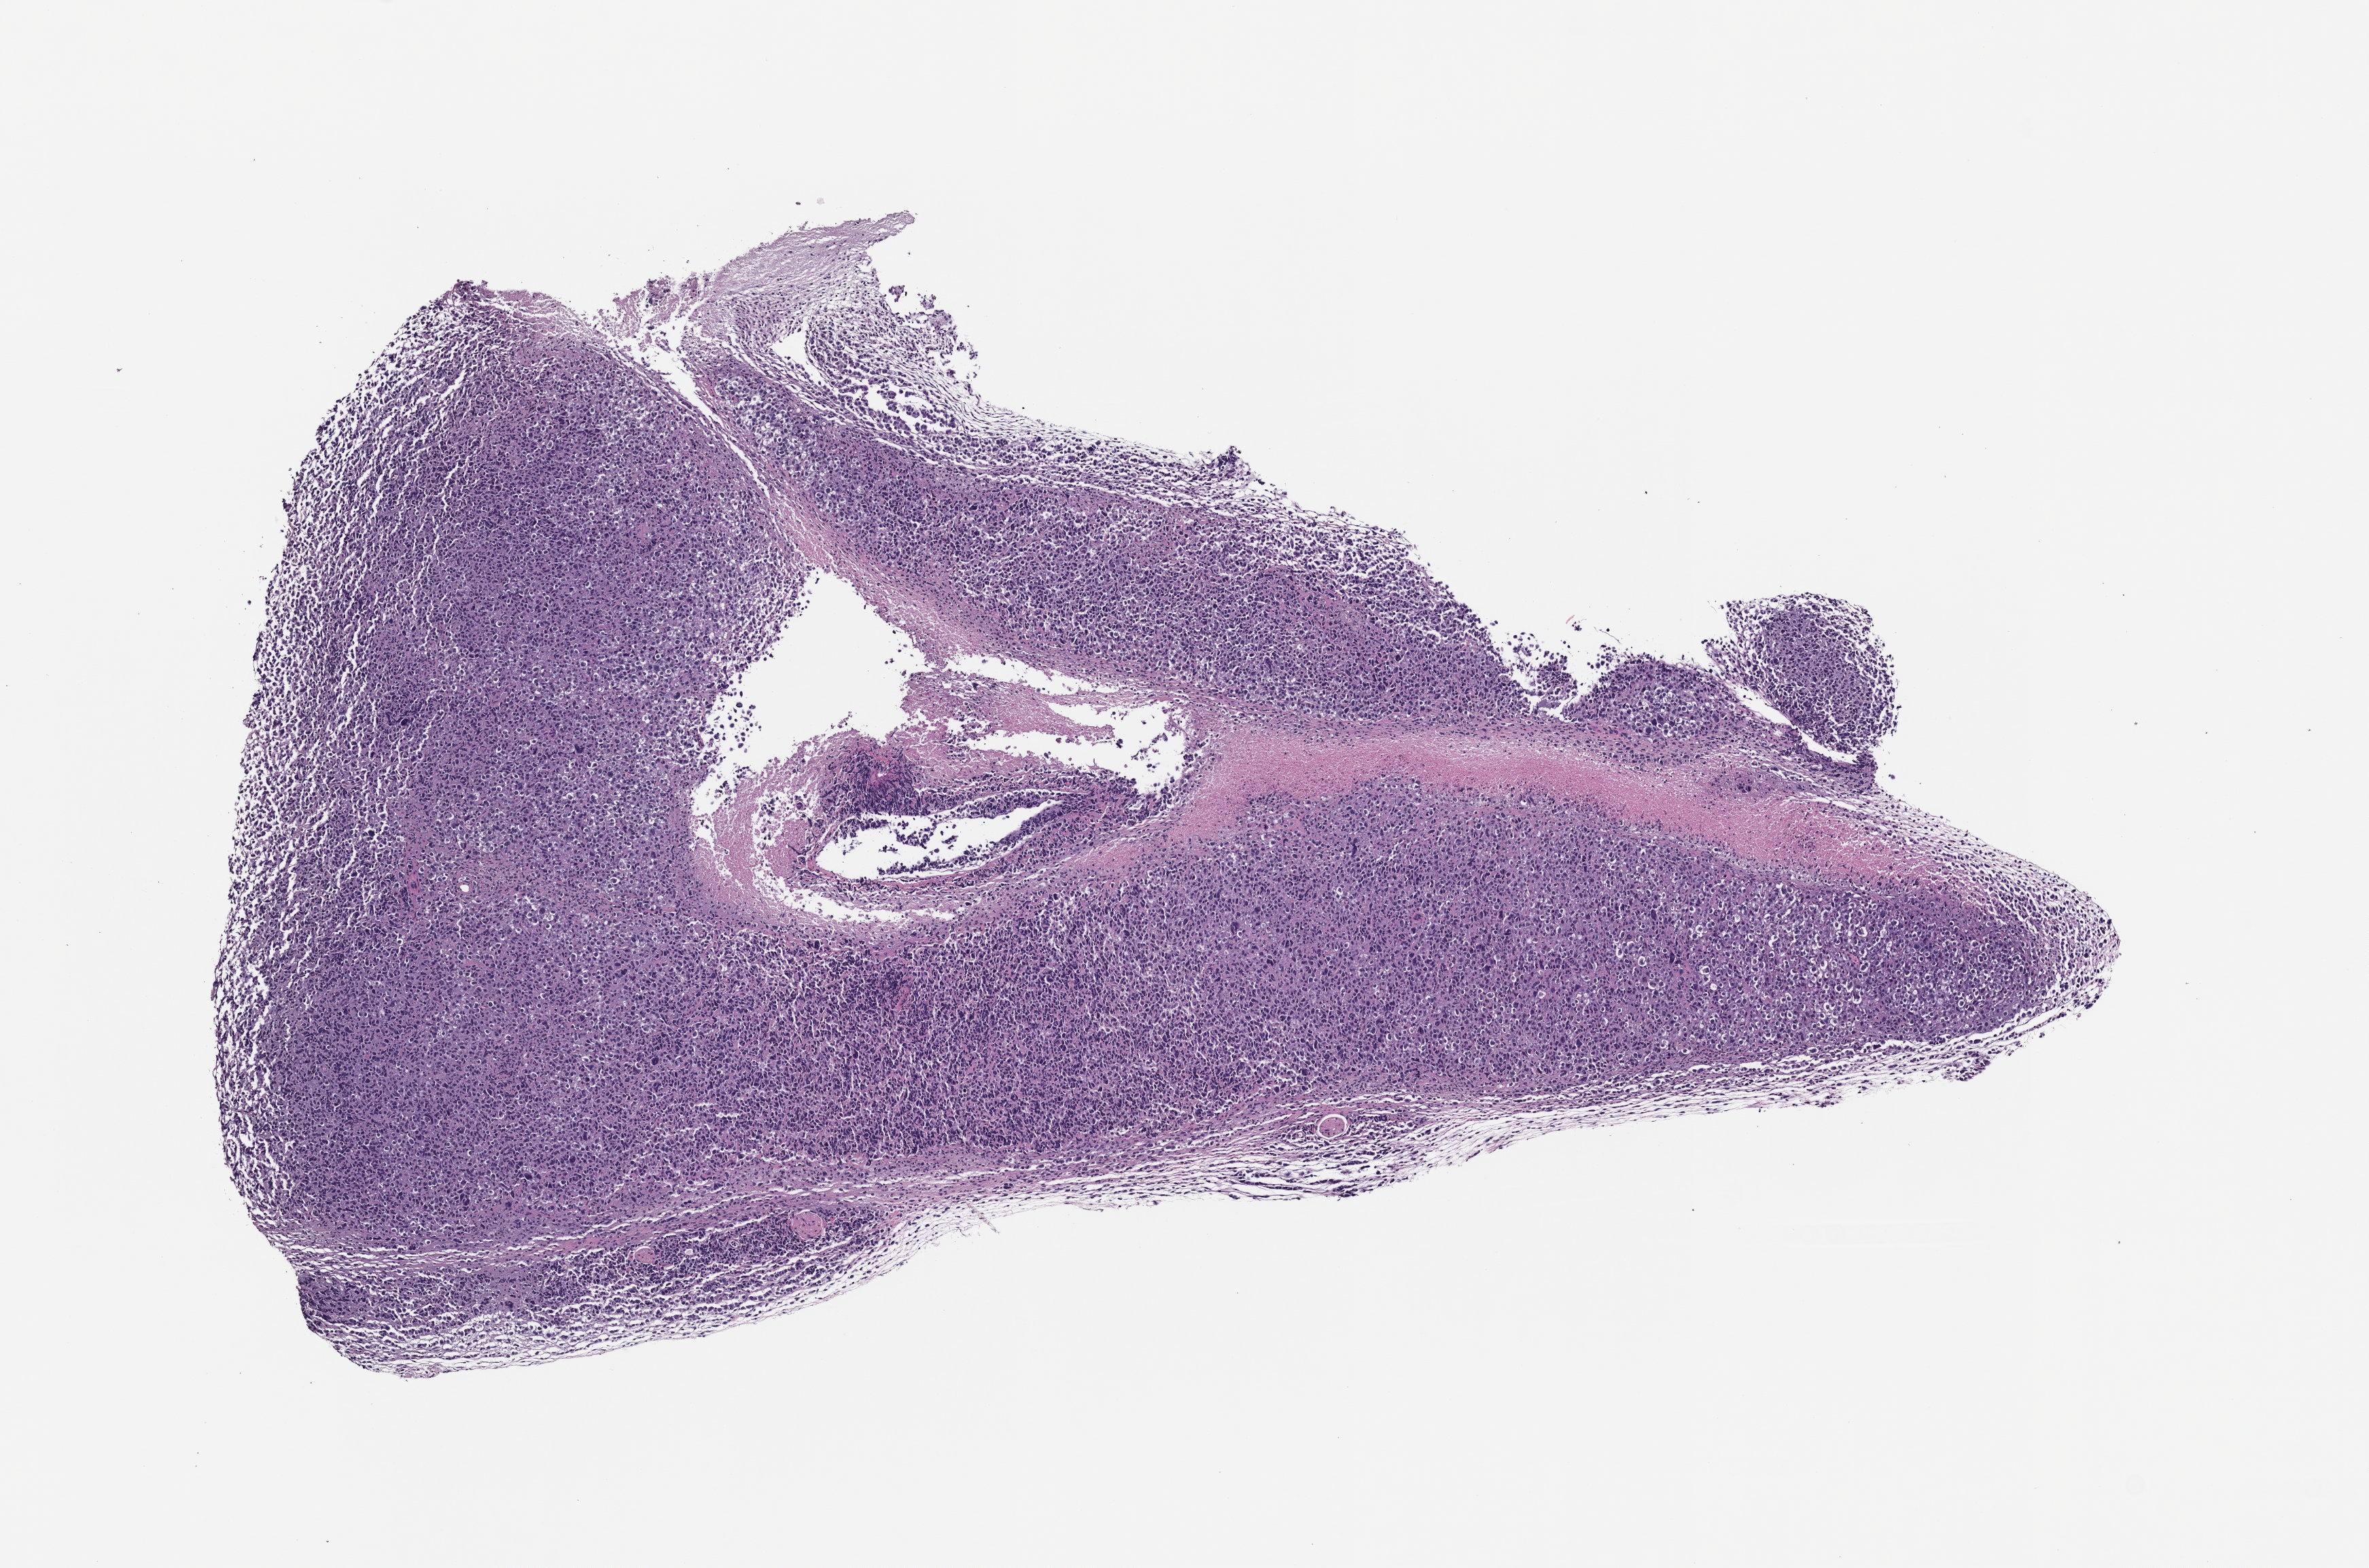
Whole-slide image, hematoxylin and eosin (H&E): patient-derived xenograft (human tumor grown in a mouse) — shown as a low-resolution overview of the whole scanned area (about 7.0 x 4.6 mm).
* specimen: formalin-fixed paraffin-embedded section